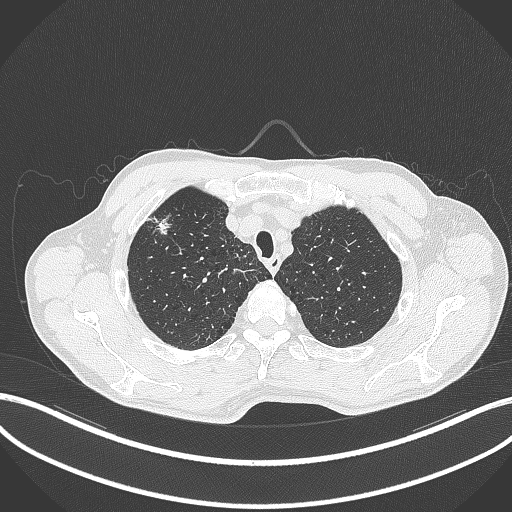
Chest CT, one axial slice; slice 356 of 427 in the series (ordered by position); 120 kVp; lung window (W 1500 / L -600 HU); 1 mm slice thickness; 512 × 512 image matrix, field of view 400 × 400 mm. Male patient, age 69 years. Case-level facts recorded for this patient, not image findings: clinical TNM (as recorded): T1b N1 M0.
Annotated regions visible in this slice (bounding box drawn by a radiologist):
- lung tumour (recorded histology: adenocarcinoma): bounding box <143,216,178,239> (left, top, right, bottom; pixels)